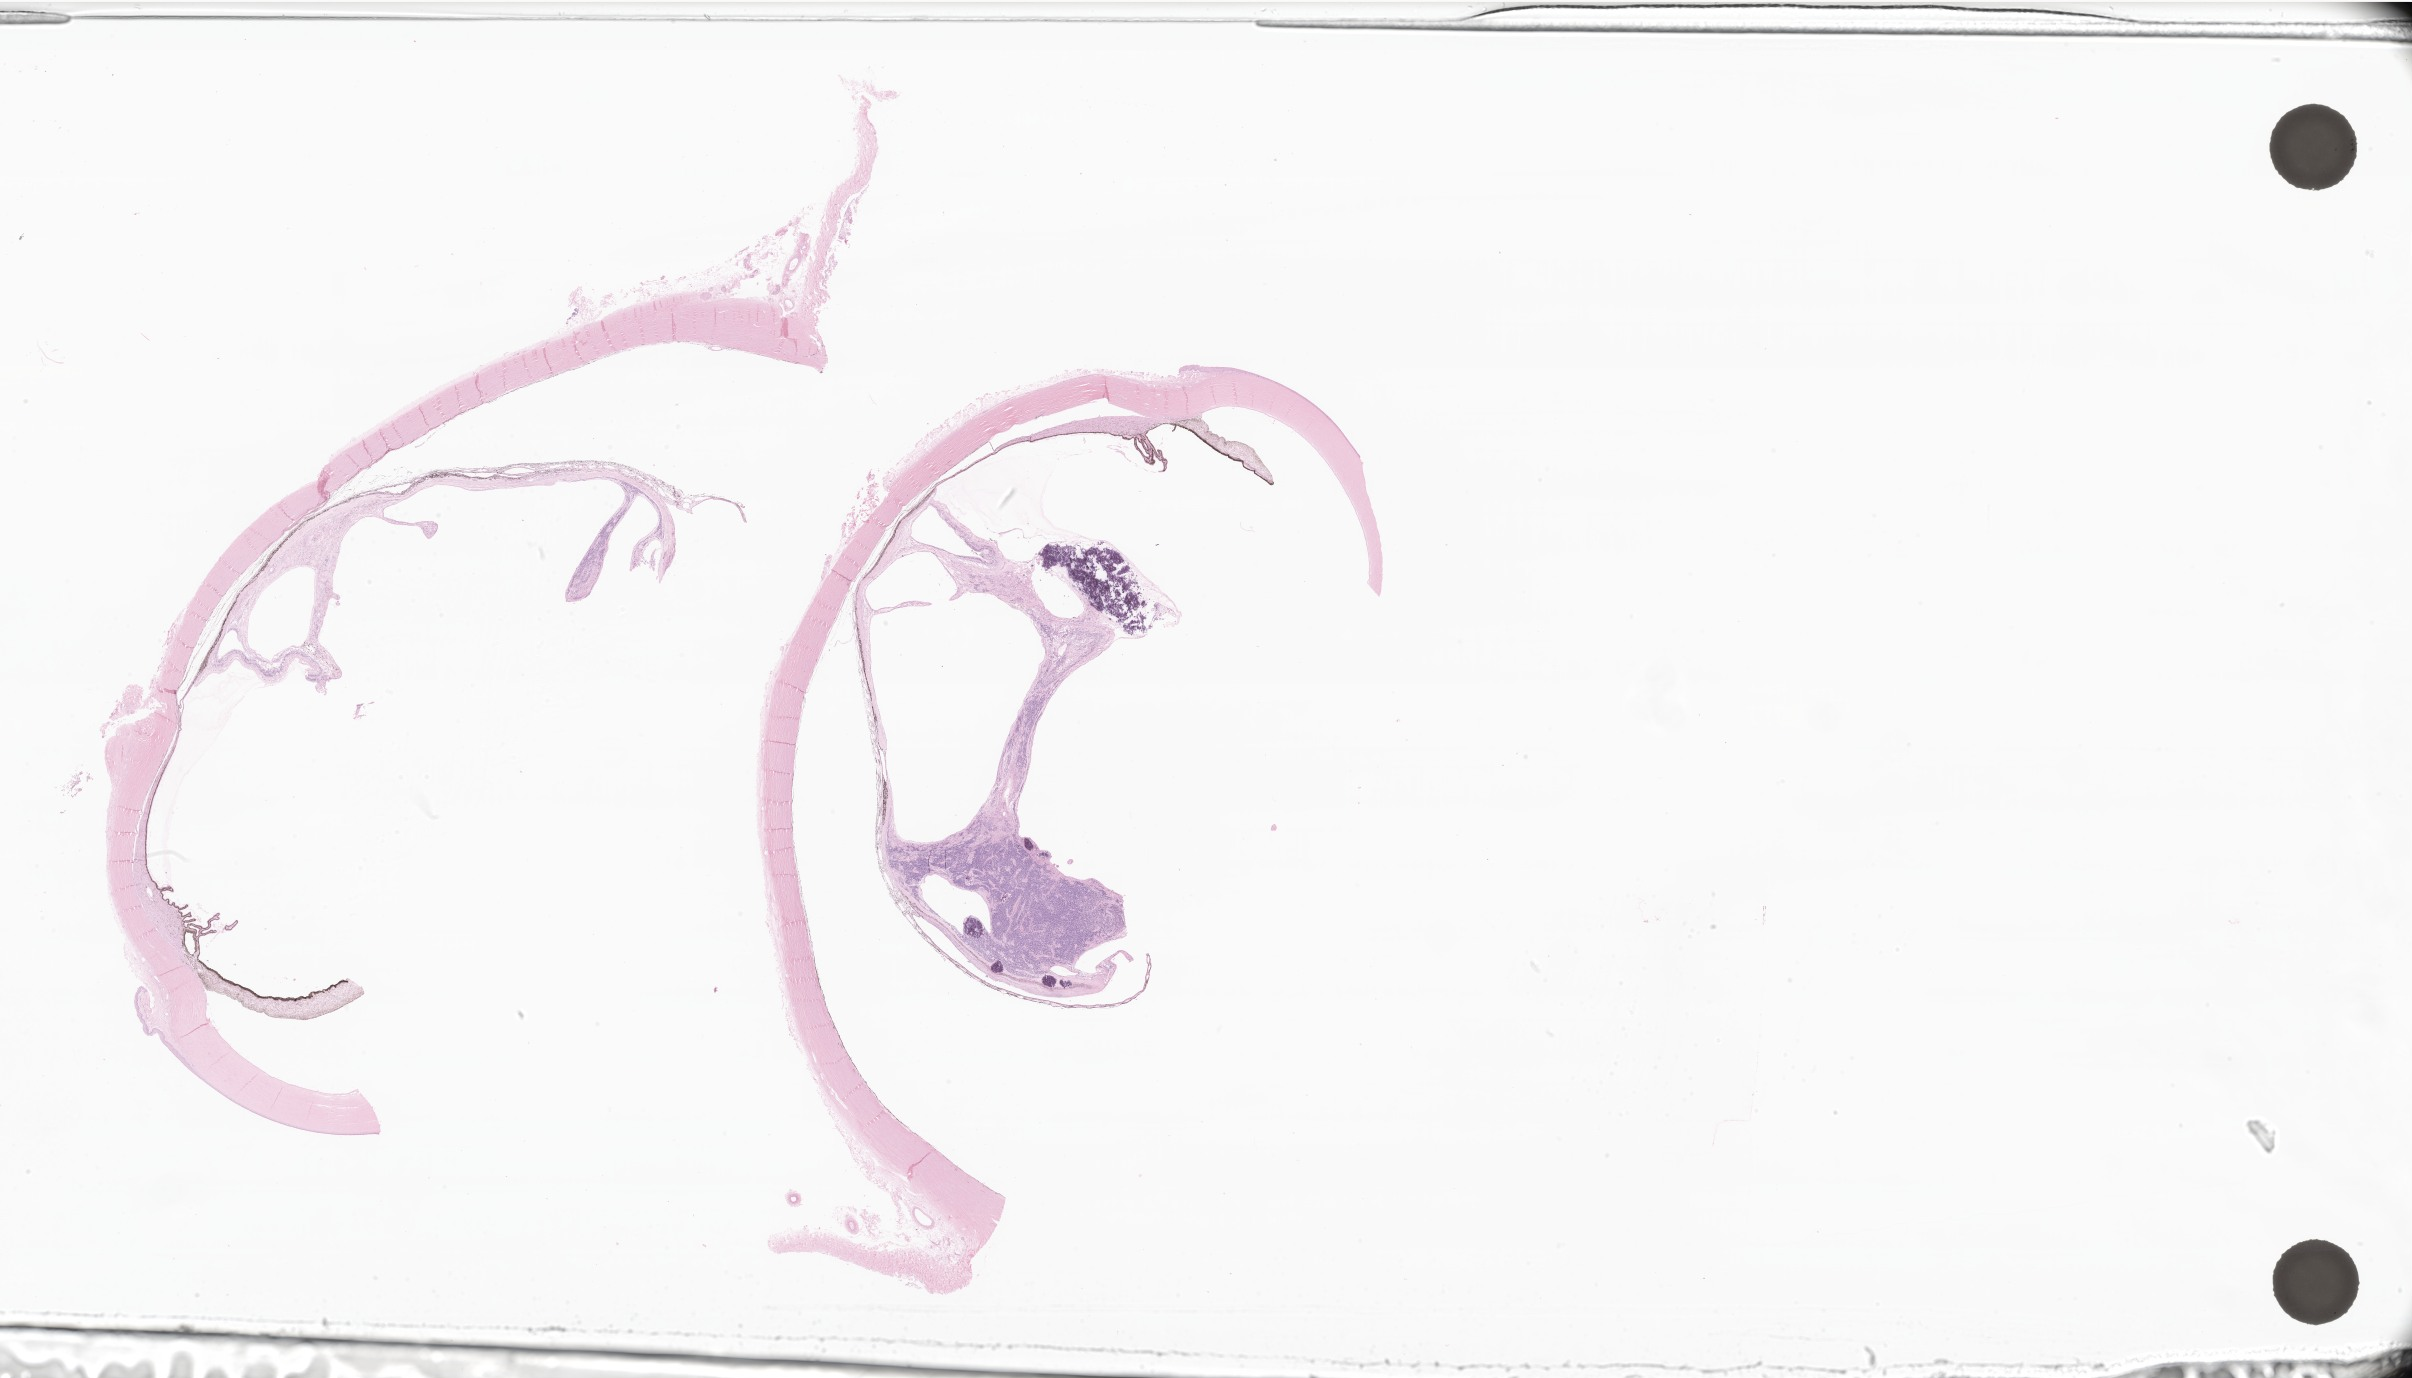
Whole-slide image, H&E stain of tumor tissue from the retina, whole scanned area (about 40.7 x 23.2 mm) shown as a low-resolution overview; FFPE section. Male patient, age 776 days (about 2.1 years).
Diagnosis (ICD-O-3 morphology term): Retinoblastoma, NOS.